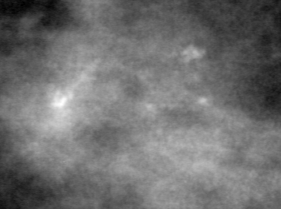
Crop from a digitized film mammogram around one marked abnormality, left breast, MLO view, BI-RADS breast density category 2 (scale 1–4).
Marked abnormality: calcifications, morphology fine linear branching, distribution linear; BI-RADS assessment category 4; pathology (as recorded): malignant.